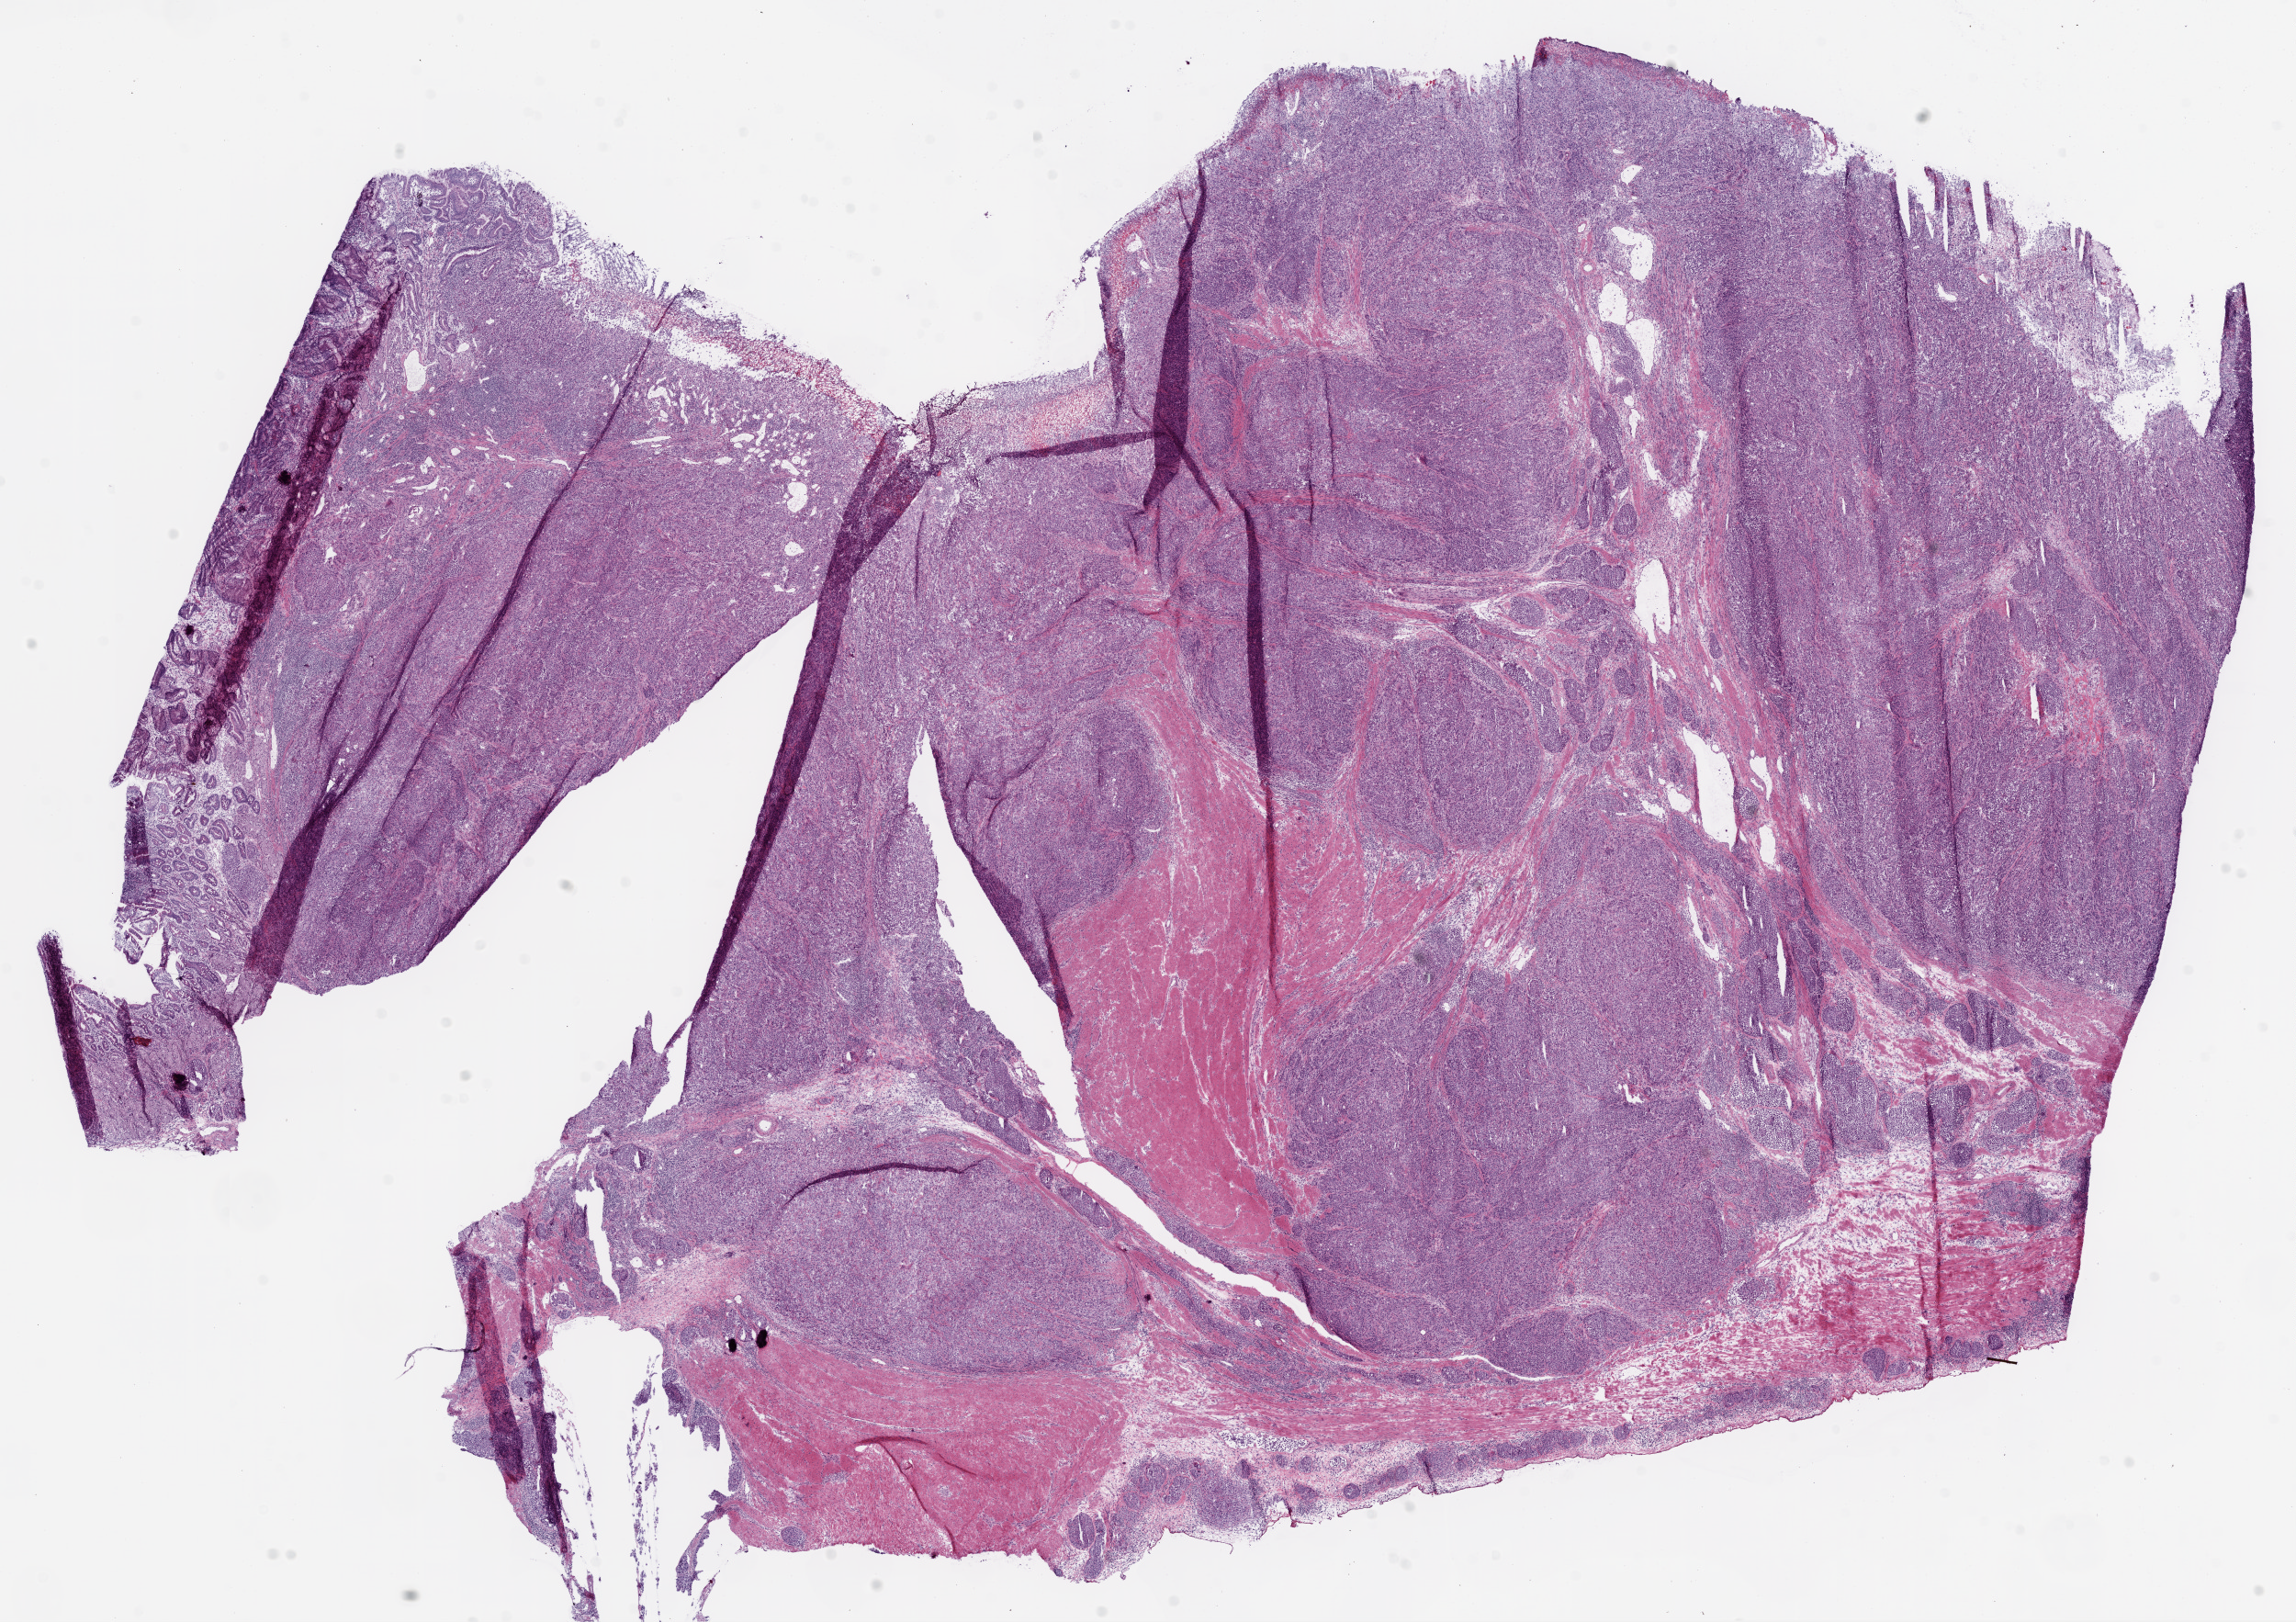
Digitized H&E-stained tissue section (whole slide), low-resolution overview of the scanned area, about 20.1 x 14.2 mm (from a 20x scan), frozen section from the bottom of the tissue portion, primary tumour sample from the stomach. Patient: female, age at initial diagnosis 78 years. Slide review estimates, as recorded: tumour cells 75%, tumour nuclei 70%.
Pathologic diagnosis: Adenocarcinoma, NOS (gastric antrum).